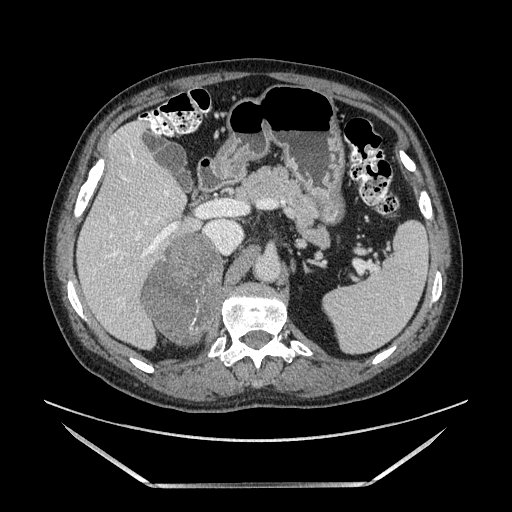
Contrast-enhanced abdominal CT, one axial slice. Slice 89 of 185 in the series (ordered by position). Soft-tissue window (W 400 / L 40 HU). 512 × 512 image matrix. Male patient. Case-level facts recorded for this patient, not image findings: diagnosis: adrenocortical carcinoma; tumour side: right adrenal; tumour size at pathology: 10.3 cm; Ki-67 index: 20 %; stage (as recorded): 3.
Structures marked on this image (semi-automatically segmented with operator editing):
- mass: bounding box (x1, y1, x2, y2) in pixels: (143, 232, 226, 344)